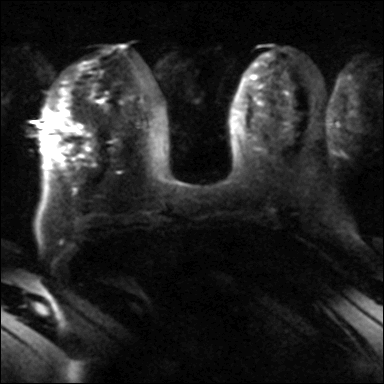
Breast MRI, one axial slice. Position 18 of 40 along the scan axis. Diffusion-weighted series; image 2 of 4 stored at this slice position (different b-values; order by instance number). 3 T. 384 × 384 image matrix, field of view 320 × 320 mm. Female patient.
Outlined on this slice (manually delineated by an expert):
- tumour on diffusion-weighted imaging: bounding box [x1, y1, x2, y2] px = [54, 141, 61, 148]